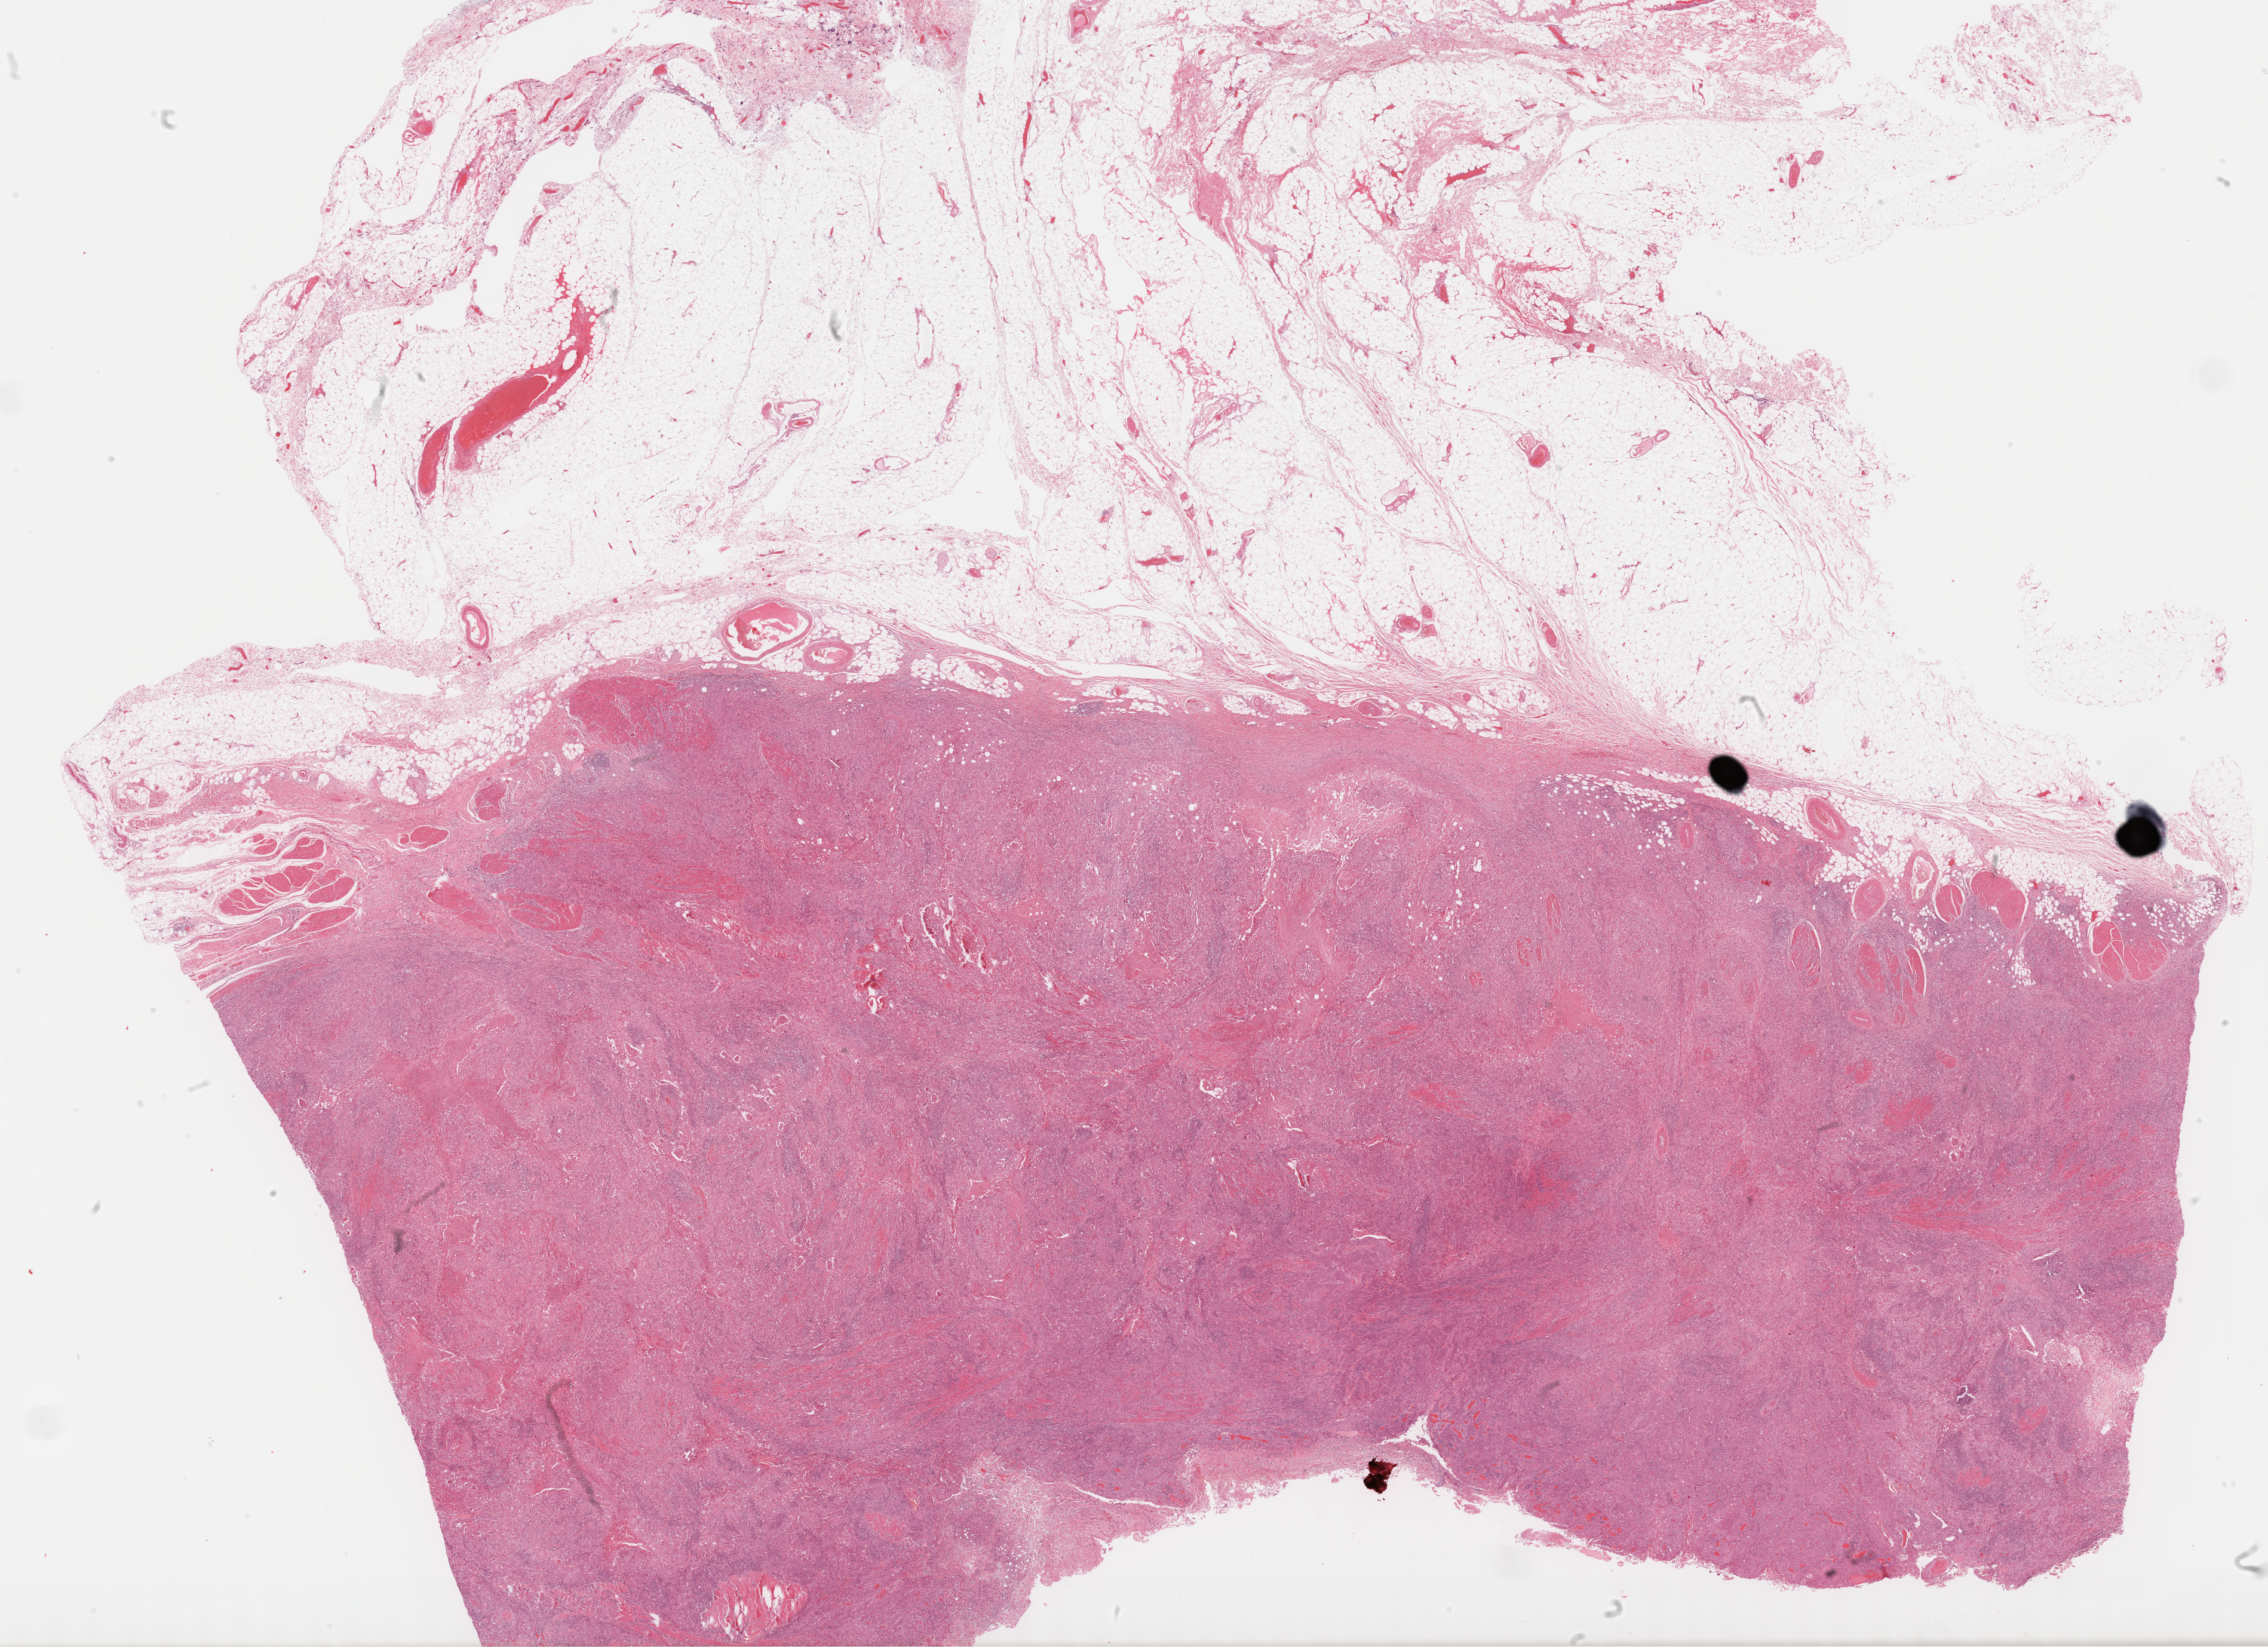
Hematoxylin and eosin (H&E) stained whole-slide image — a low-resolution overview of the entire scanned area, about 30.7 x 22.3 mm (acquisition: 40x scan), formalin-fixed paraffin-embedded (FFPE) diagnostic section, sample: primary tumour, bladder. Female patient; age at initial diagnosis 70 years. Histologic grade: high grade.
TNM: T3b N0 MX. AJCC pathologic stage: III (7th edition). Histologic diagnosis: Transitional cell carcinoma (lateral wall of bladder). Lymph nodes positive (case pathology): 0 of 15 examined.